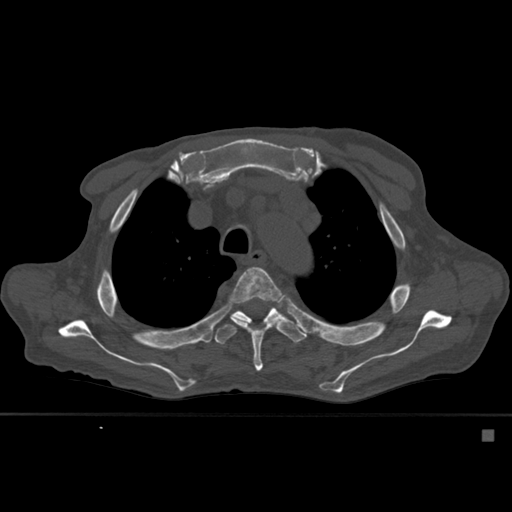
CT including the spine, one axial slice. Slice 411 of 527 in the series (ordered by position). Bone window (W 1800 / L 400 HU). 1.5 mm slice thickness. 512 × 512 image matrix, field of view 373 × 373 mm. Male patient, age 78 years. Case-level facts recorded for this patient, not image findings: primary cancer: prostate.
Outlined on this slice (semi-automatic segmentation, software-assisted and operator-edited):
- T4 vertebra: bounding box <228,267,284,371> (left, top, right, bottom; pixels)
- T5 vertebra: <214,301,307,345>